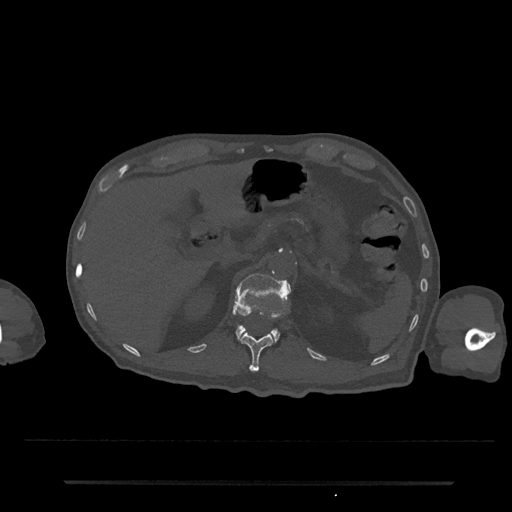
CT including the spine, one axial slice; position 170 of 797 along the scan axis; reconstruction kernel Br40s/3; bone window (W 1800 / L 400 HU); 0.5 mm slice thickness; 512 × 512 image matrix, field of view 427 × 427 mm. Male patient, age 74 years. From the clinical record (not read from this slice): primary cancer: prostate.
Structures marked on this image (semi-automatic segmentation, software-assisted and operator-edited):
- L1 vertebra: bounding box (x1, y1, x2, y2) in pixels: (233, 273, 292, 343)
- T12 vertebra: (240, 333, 274, 372)